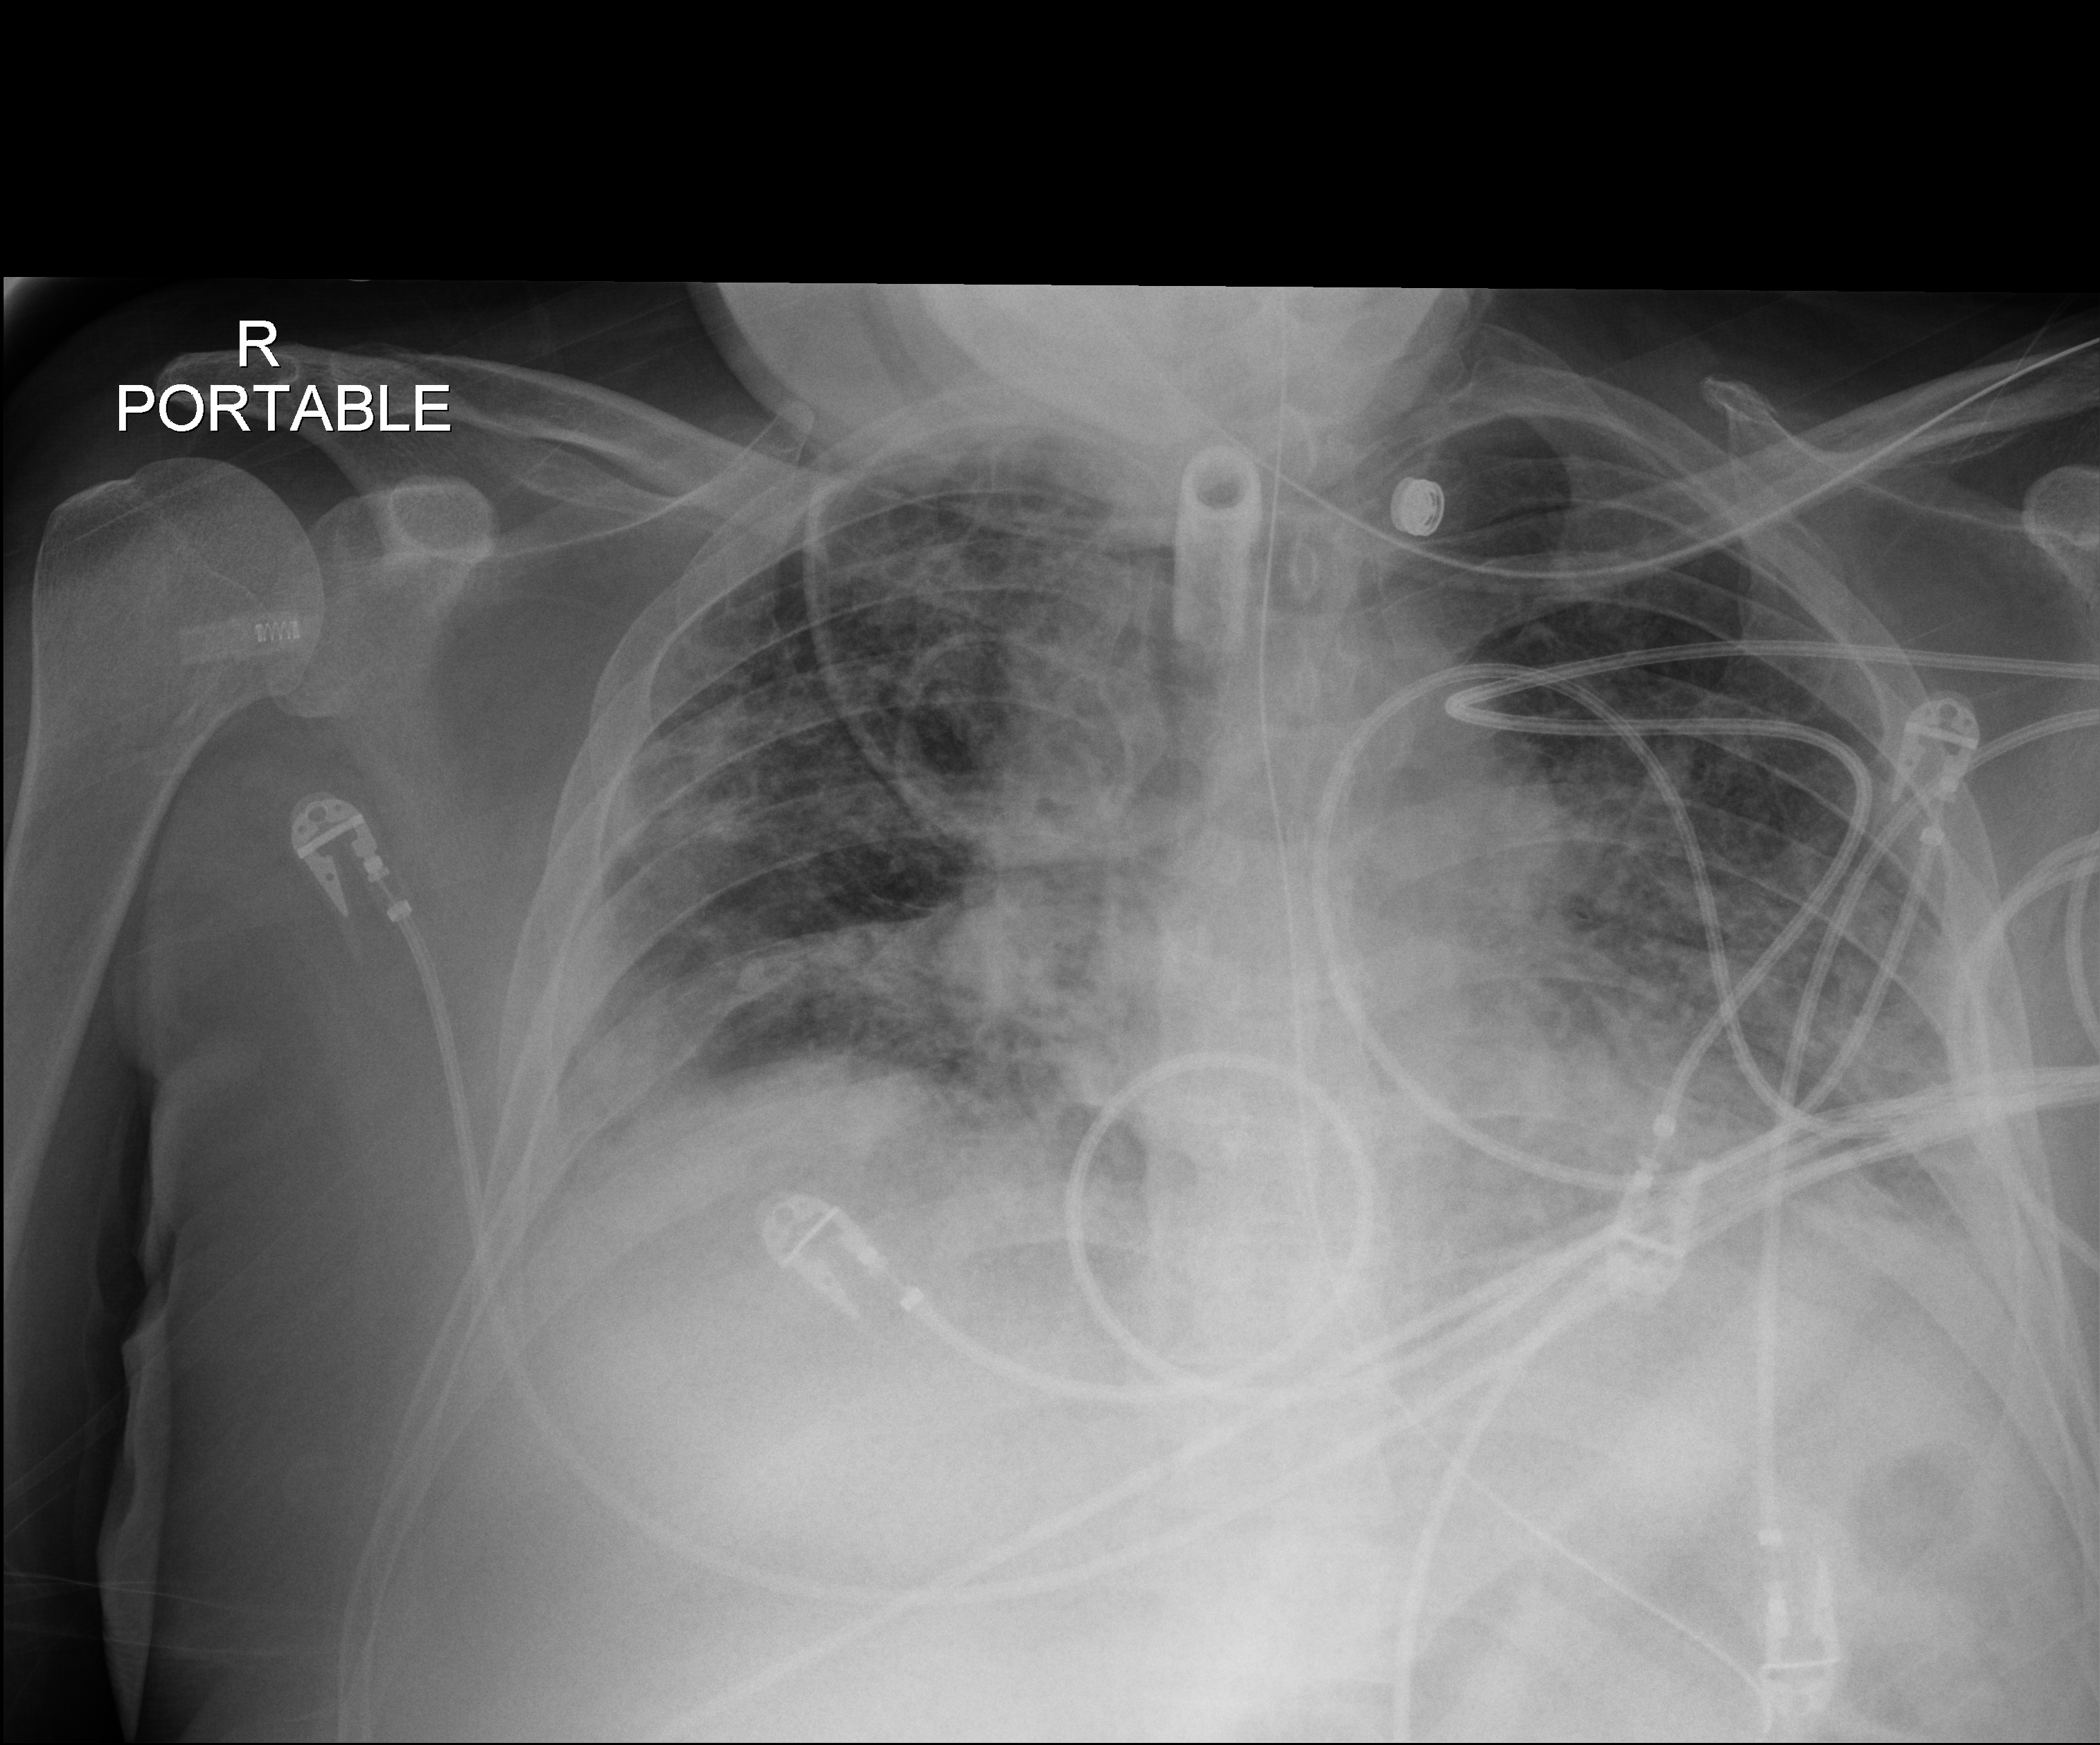
Portable chest radiograph. Patient hospitalised with COVID-19; male, aged 18–59 years.
Admission-level facts for this patient (not findings on this image; timing relative to this image not recorded): mechanically ventilated during this hospital stay: yes; admitted to intensive care during this hospital stay: yes.